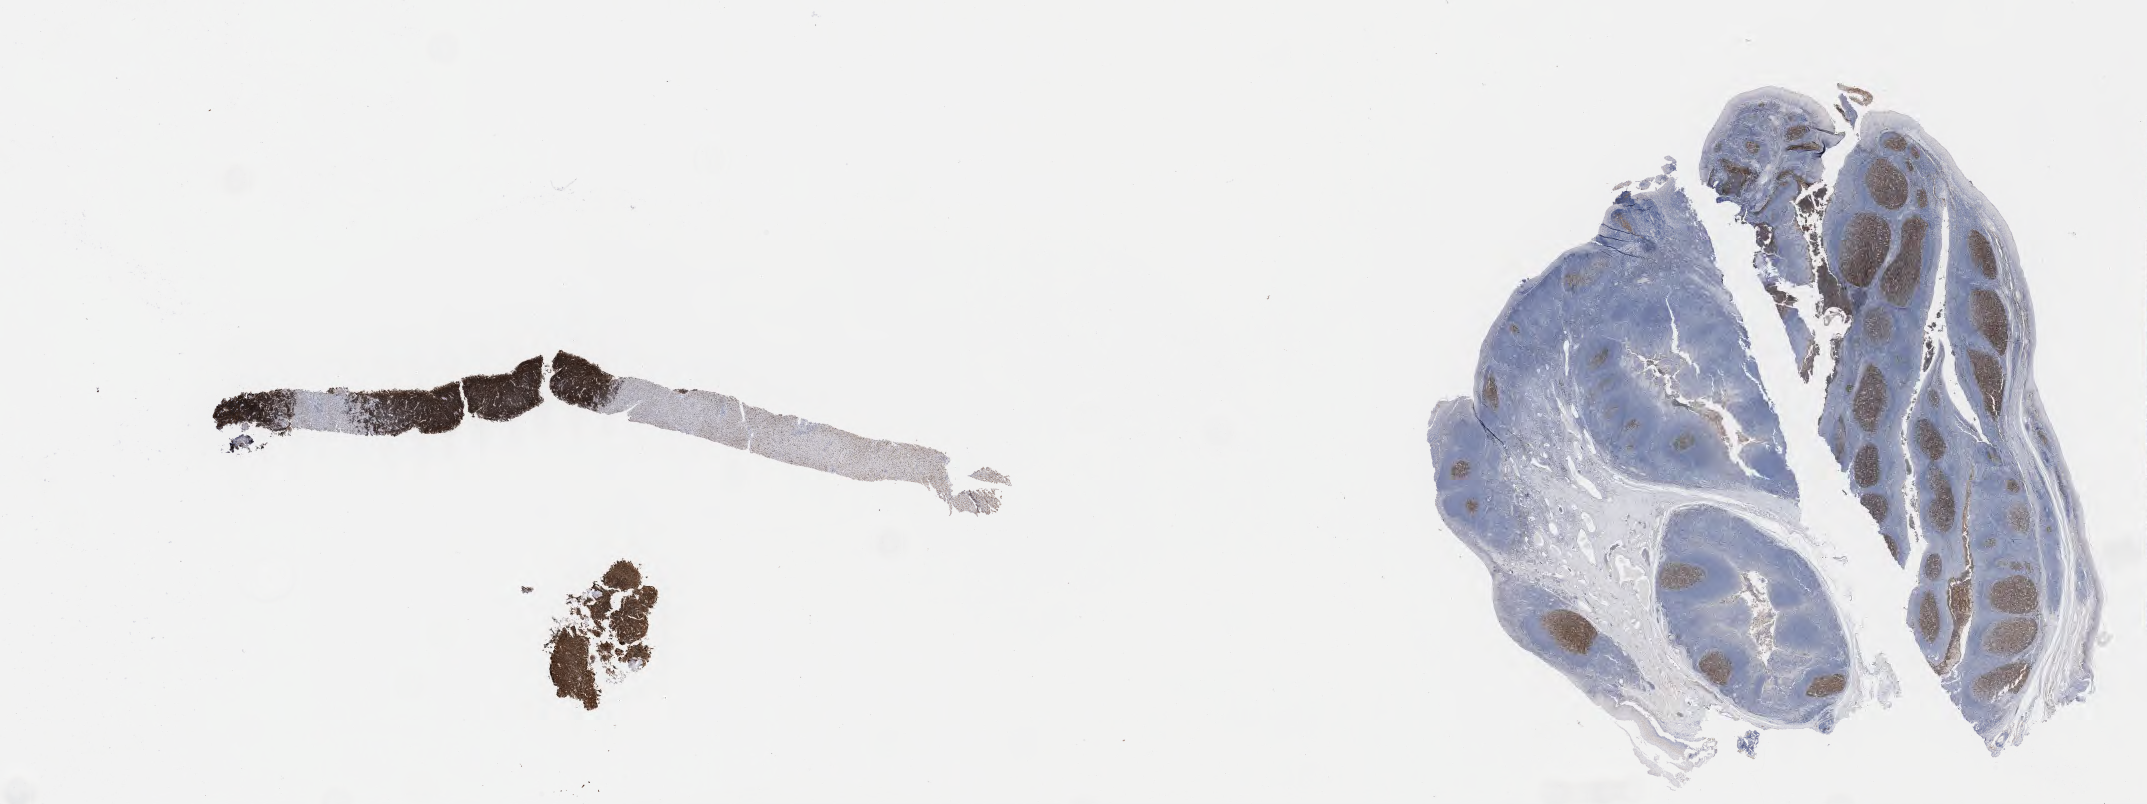
Immunohistochemistry (IHC) whole-slide image stained for CD10 — whole scanned area (about 34.7 x 13.0 mm) shown as a low-resolution overview, specimen: tumor tissue. Patient male; 68 years old.
Diagnosis: Burkitt lymphoma, NOS.